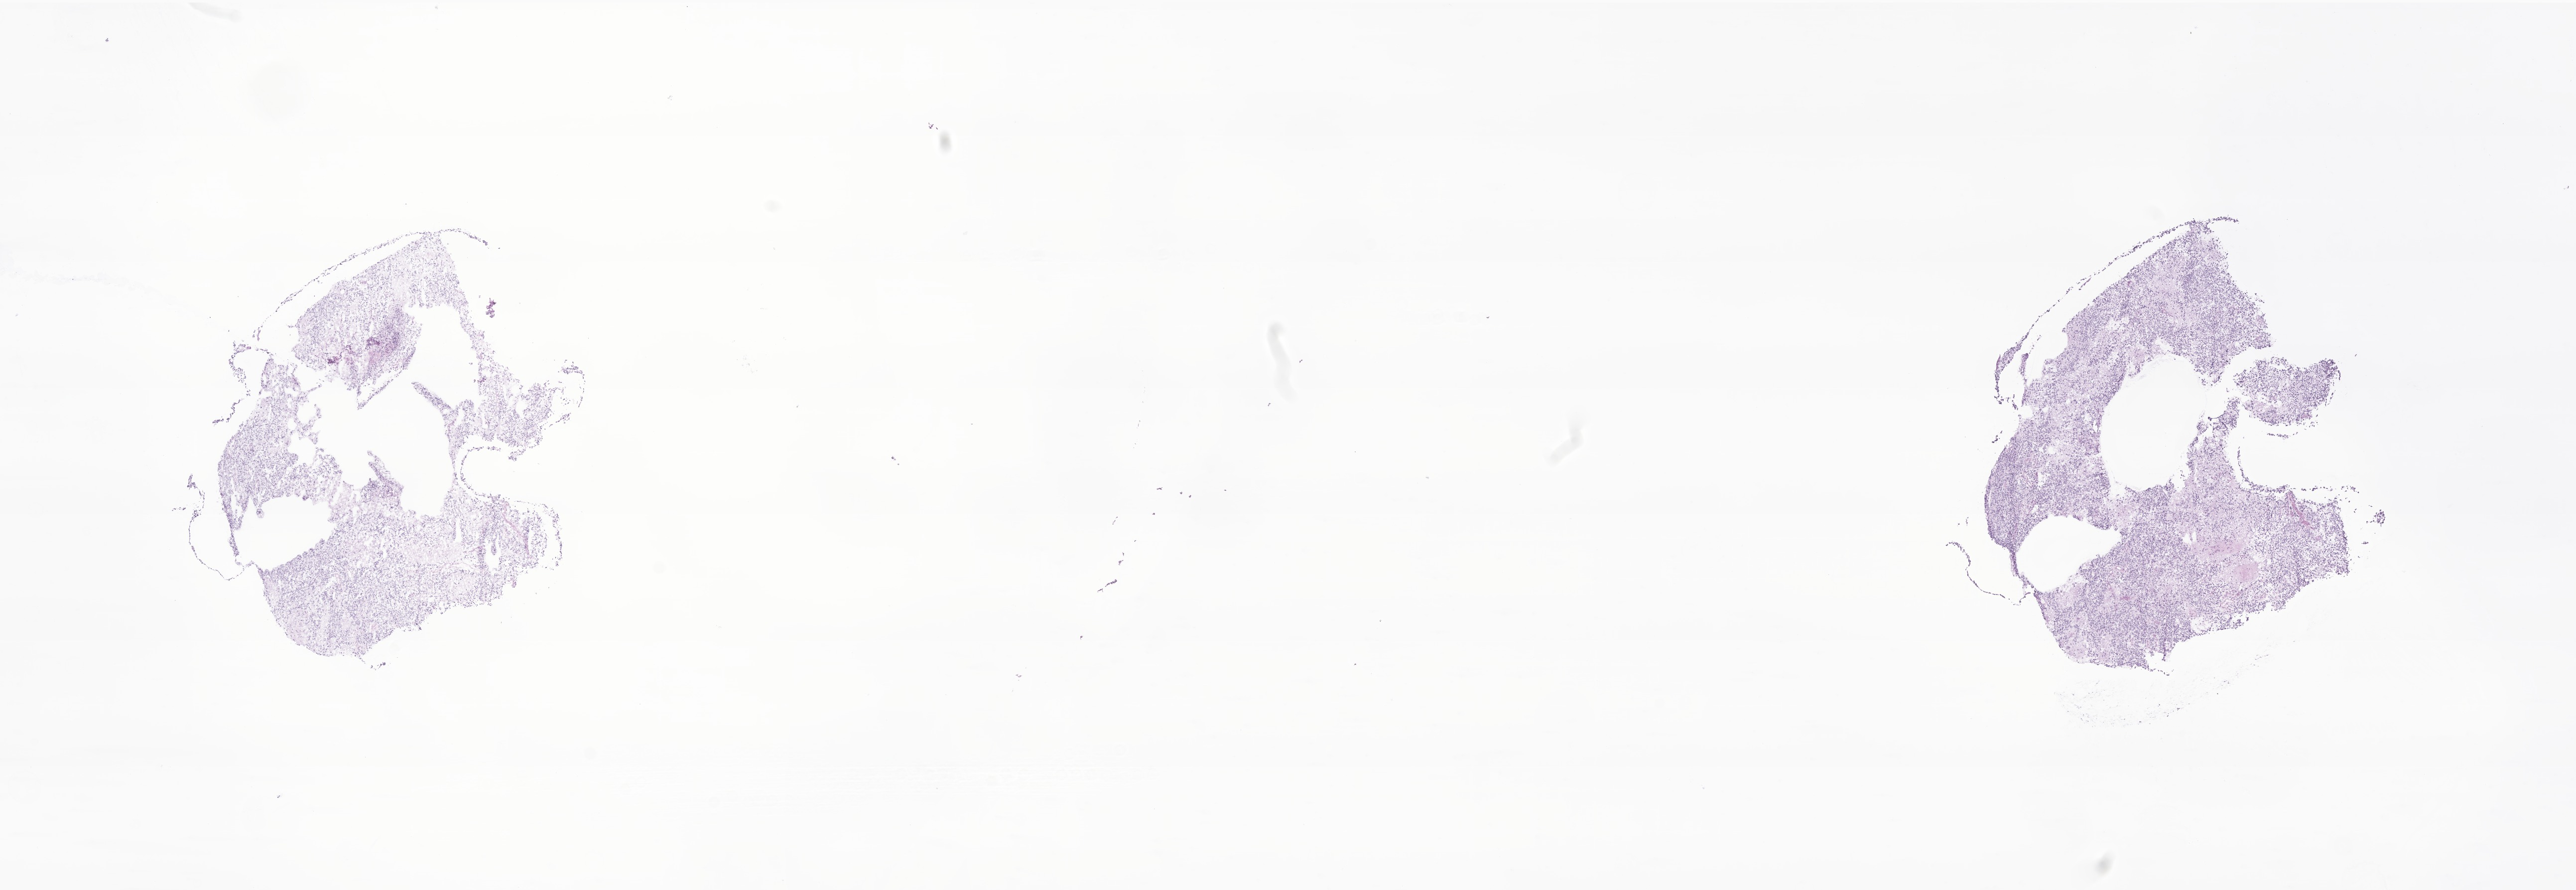
Digitized haematoxylin and eosin-stained section of tumor tissue from the brain, shown as a low-resolution overview of the whole scanned area (about 21.8 x 7.5 mm). Frozen section (OCT-embedded). Patient: male, age 165 months.
Recorded diagnosis: Neoplasm, malignant.